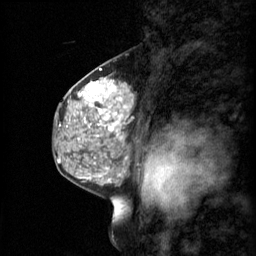
Breast MRI (dynamic contrast-enhanced), one sagittal slice. Position 36 of 60 along the scan axis. 3 images stored at this slice position (order not interpretable as contrast timing). 1.5 T. TE 4.2 ms, TR 11 ms. 2 mm slice thickness. 256 × 256 image matrix, field of view 200 × 200 mm. Female patient, age 48 years.
Structures marked on this image (semi-automatic segmentation, software-assisted and operator-edited):
- analysis volume of interest (the breast-tissue region the enhancement analysis was run in; not a lesion): box from (x=69, y=74) to (x=134, y=147) px
- tumour enhancement mask (voxels above the 70 % enhancement threshold inside the analysis volume of interest): (x=78, y=78)–(x=134, y=141)